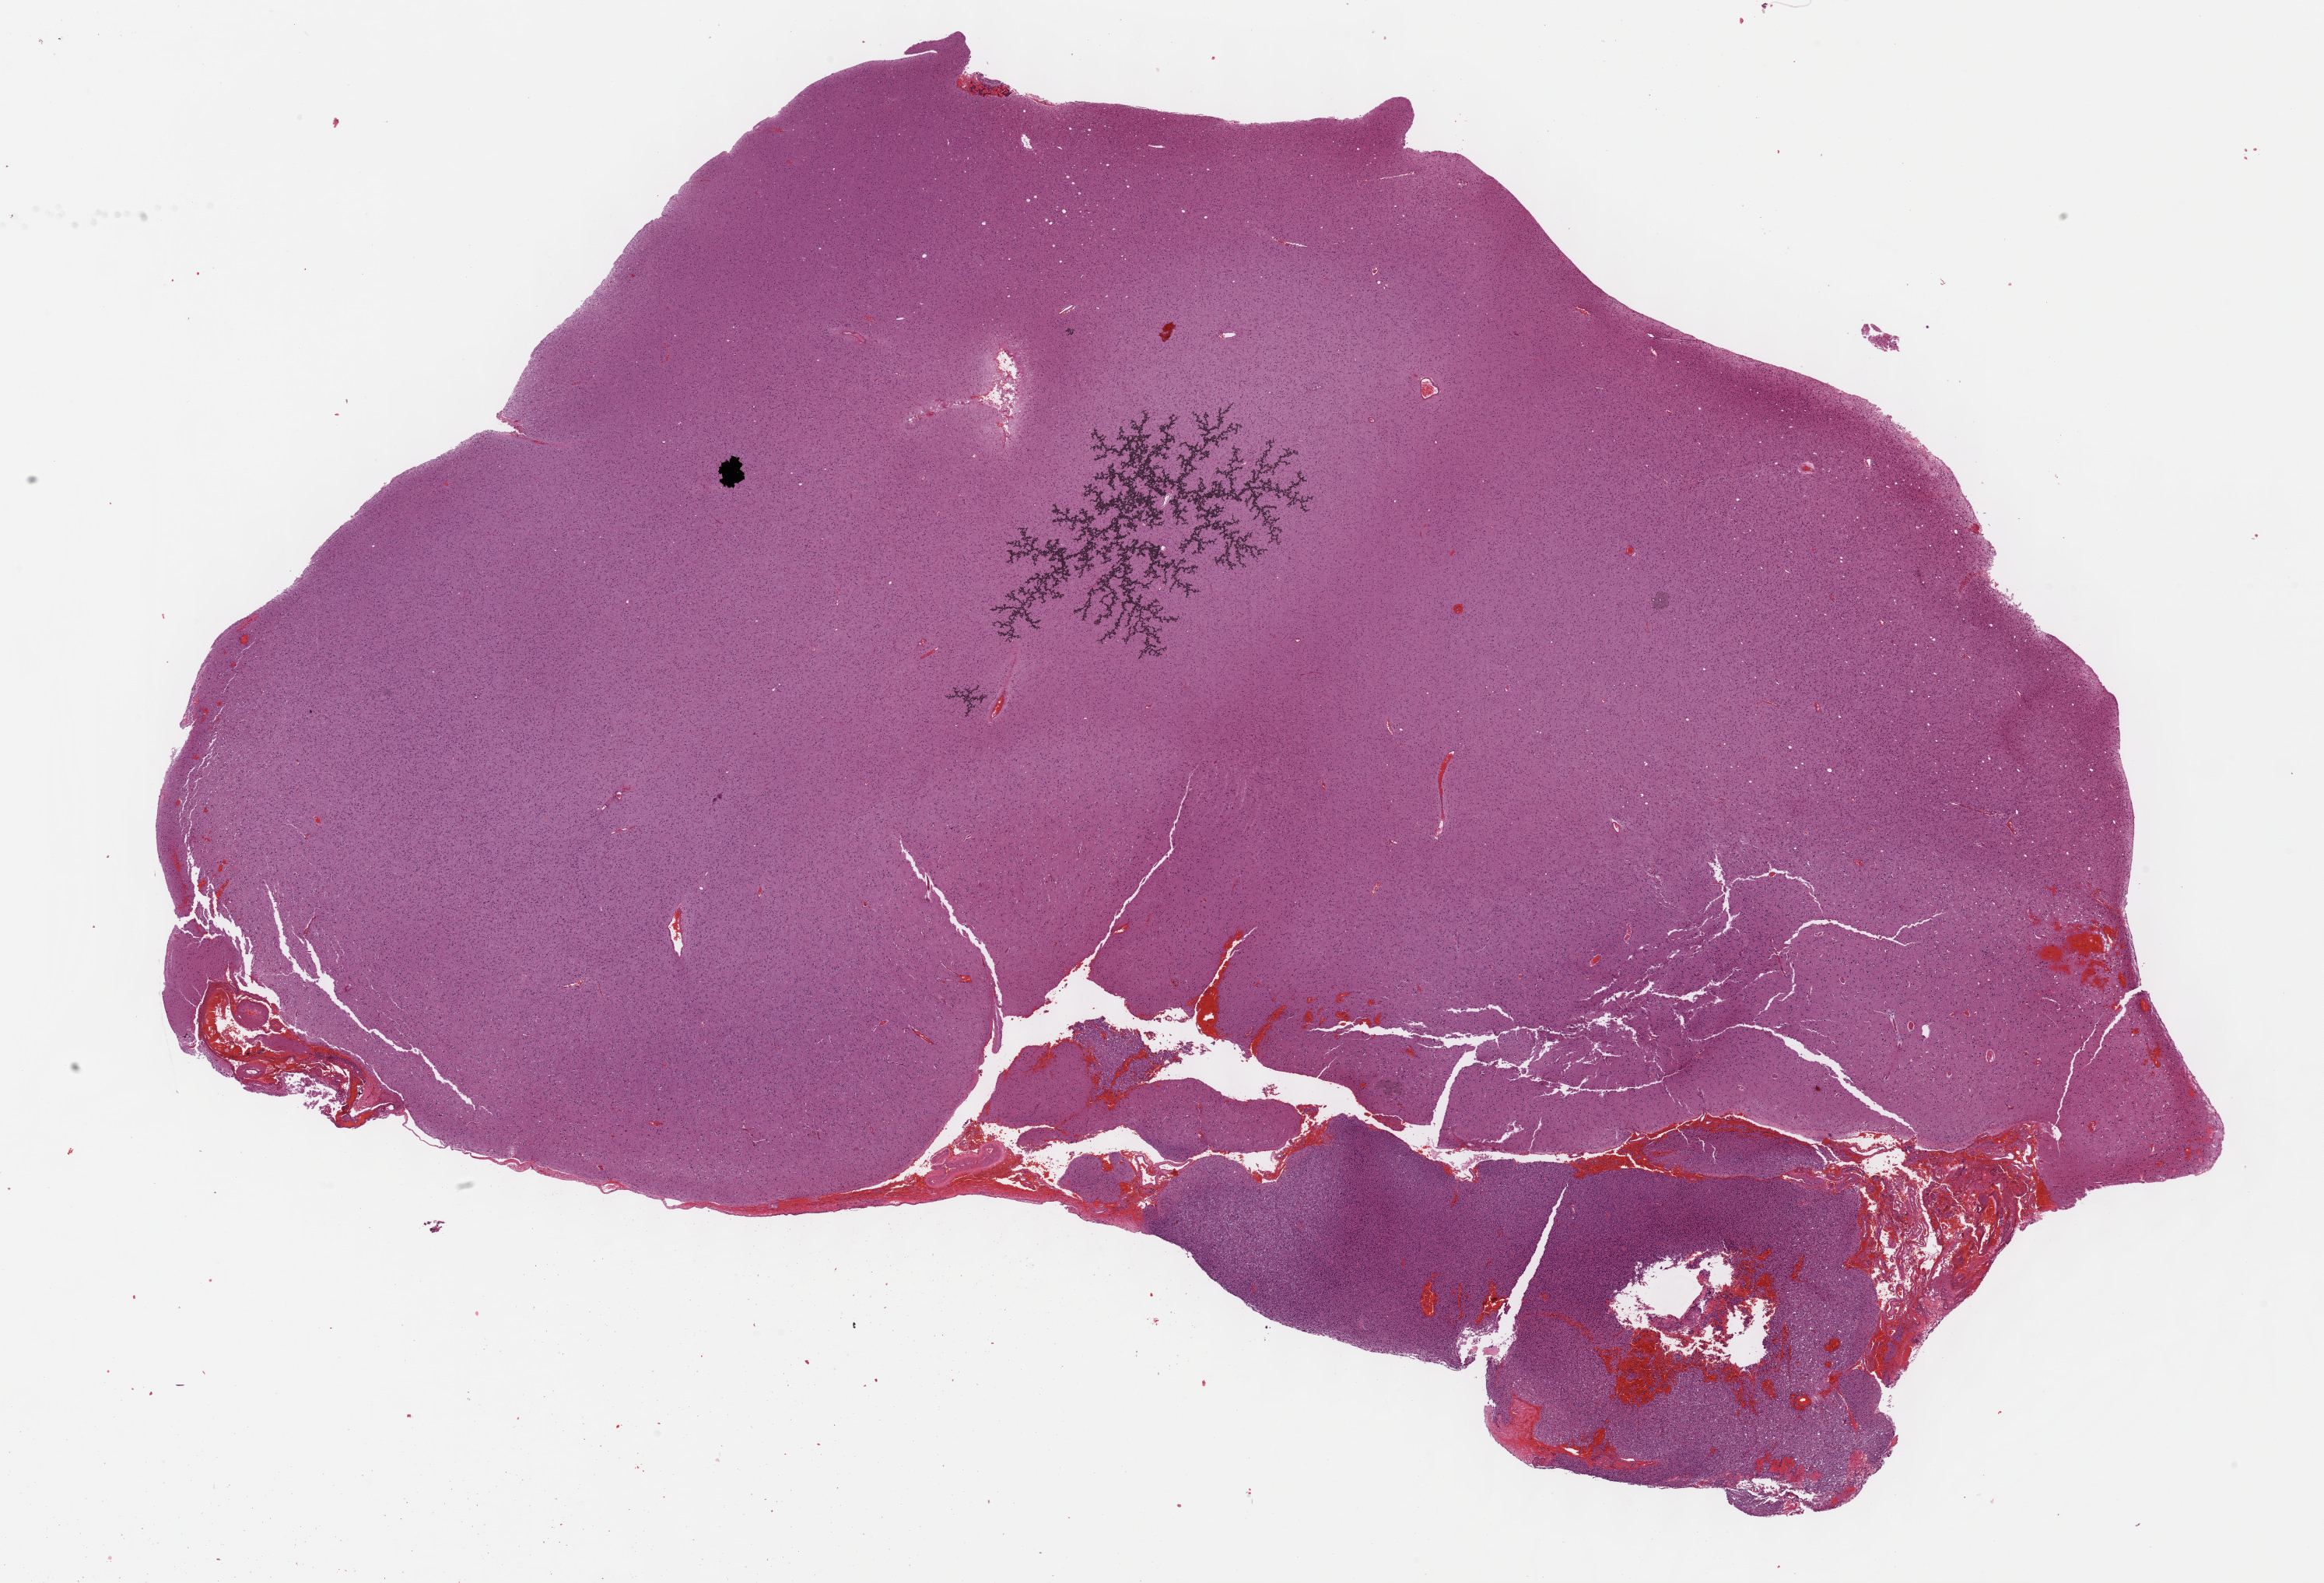
Digitized H&E tissue section (whole slide), a low-resolution overview of the entire scanned area, about 24.2 x 16.5 mm (acquisition: 40x scan). FFPE section. Primary tumour sample from the brain. Patient: male, age at initial diagnosis 34 years. Histologic grade: G3 (poorly differentiated).
• diagnosis: Mixed glioma (cerebrum)